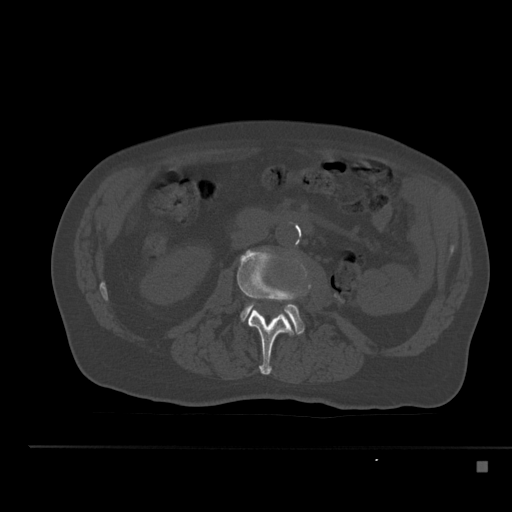
CT including the spine, one axial slice; slice 178 of 517 in the series (ordered by position); 120 kVp; bone window (W 1800 / L 400 HU); 1.5 mm slice thickness; 512 × 512 image matrix, field of view 408 × 408 mm. Male patient, age 70 years. From the clinical record (not read from this slice): primary cancer: renal.
Annotated regions visible in this slice (semi-automatic segmentation, software-assisted and operator-edited):
- L2 vertebra: bounding box [x1, y1, x2, y2] px = [237, 248, 302, 375]
- L3 vertebra: [240, 303, 304, 334]